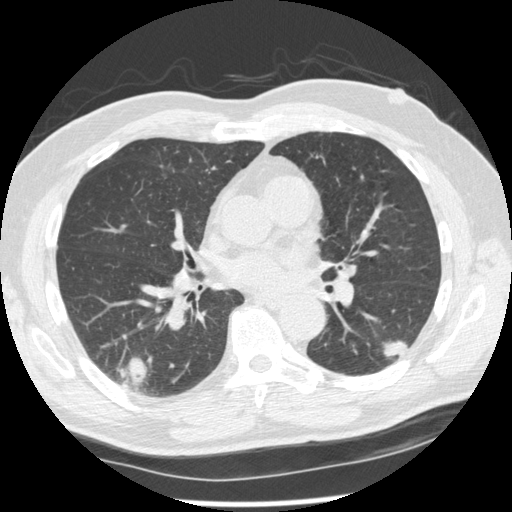
Axial slice from a low-dose chest CT screening exam. Second annual screen. Lung window (W 1500 / L -600 HU). 1.25 mm slice thickness. Standard (soft-tissue) reconstruction kernel (STANDARD). Slice 123 of 227 in the series. Male, age 74 years at enrolment. Former smoker at enrolment.
Expert-annotated lung lesion, bounding box (x1, y1, x2, y2) in pixels: (367, 313, 425, 368). The screening reader recorded 7 non-calcified nodules or masses ≥4 mm on this exam; which of them this box marks is not recorded. Later outcome: lung cancer diagnosed 43 days after this screen — squamous cell carcinoma, NOS, left lower lobe, well differentiated (G1), stage IA (AJCC 6th edition), 28 mm at pathology.